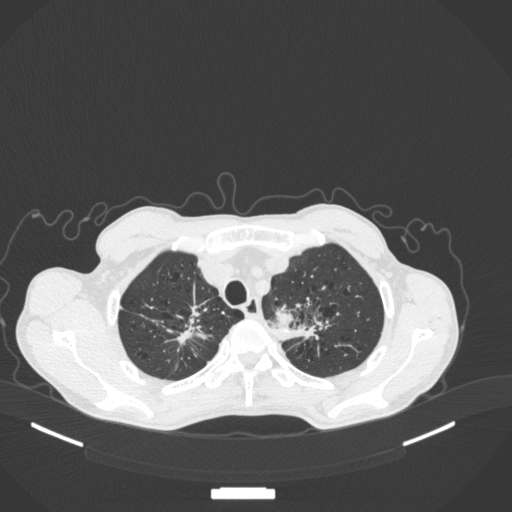
Chest CT, one axial slice; reconstruction kernel B31f; 120 kVp; lung window (W 1500 / L -600 HU); 1 mm slice thickness; 512 × 512 image matrix. Patient: male, 65 years. Case-level facts recorded for this patient, not image findings: clinical TNM (as recorded): T2b N0 M0; histopathological grade: G2.
Structures marked on this image (bounding box drawn by a radiologist):
- lung tumour (recorded histology: adenocarcinoma): box from (x=270, y=306) to (x=296, y=335) px